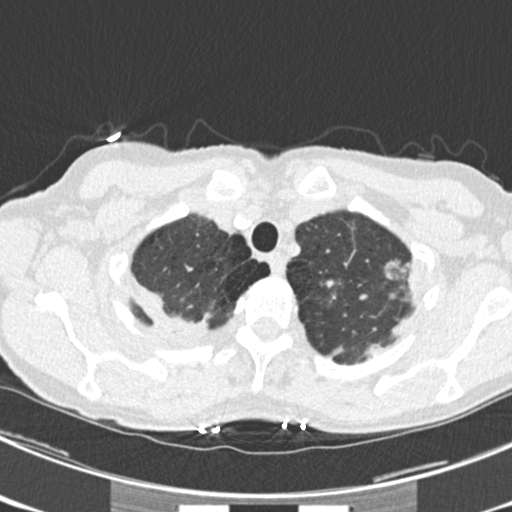
Low-dose screening chest CT, one axial slice. Position 190 of 225 along the scan axis. 120 kVp. Lung window (W 1500 / L -600 HU). 2 mm slice thickness. 512 × 512 image matrix, field of view 302 × 302 mm.
Structures marked on this image (manually delineated by an expert):
- lesion 4 (tumor, upper lobe of right lung): bounding box [x1, y1, x2, y2] px = [157, 317, 208, 345]